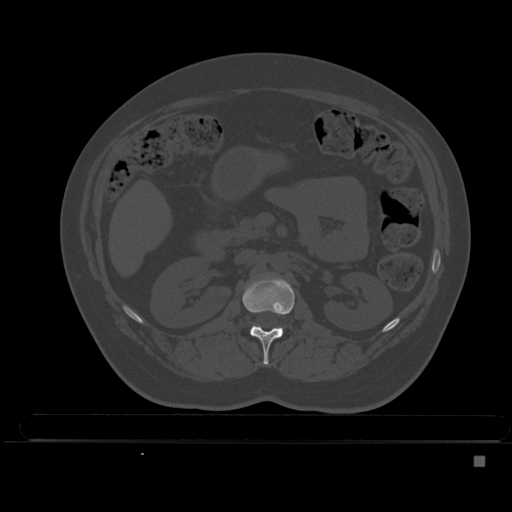
CT including the spine, one axial slice. Slice 189 of 495 in the series (ordered by position). Bone window (W 1800 / L 400 HU). 512 × 512 image matrix, field of view 404 × 404 mm. Female patient, age 33 years. Case-level facts recorded for this patient, not image findings: primary cancer: breast; vertebrae with lytic lesions (as recorded): T1.
Structures marked on this image (semi-automatic segmentation, software-assisted and operator-edited):
- L1 vertebra: bounding box (x1, y1, x2, y2) in pixels: (242, 275, 295, 365)